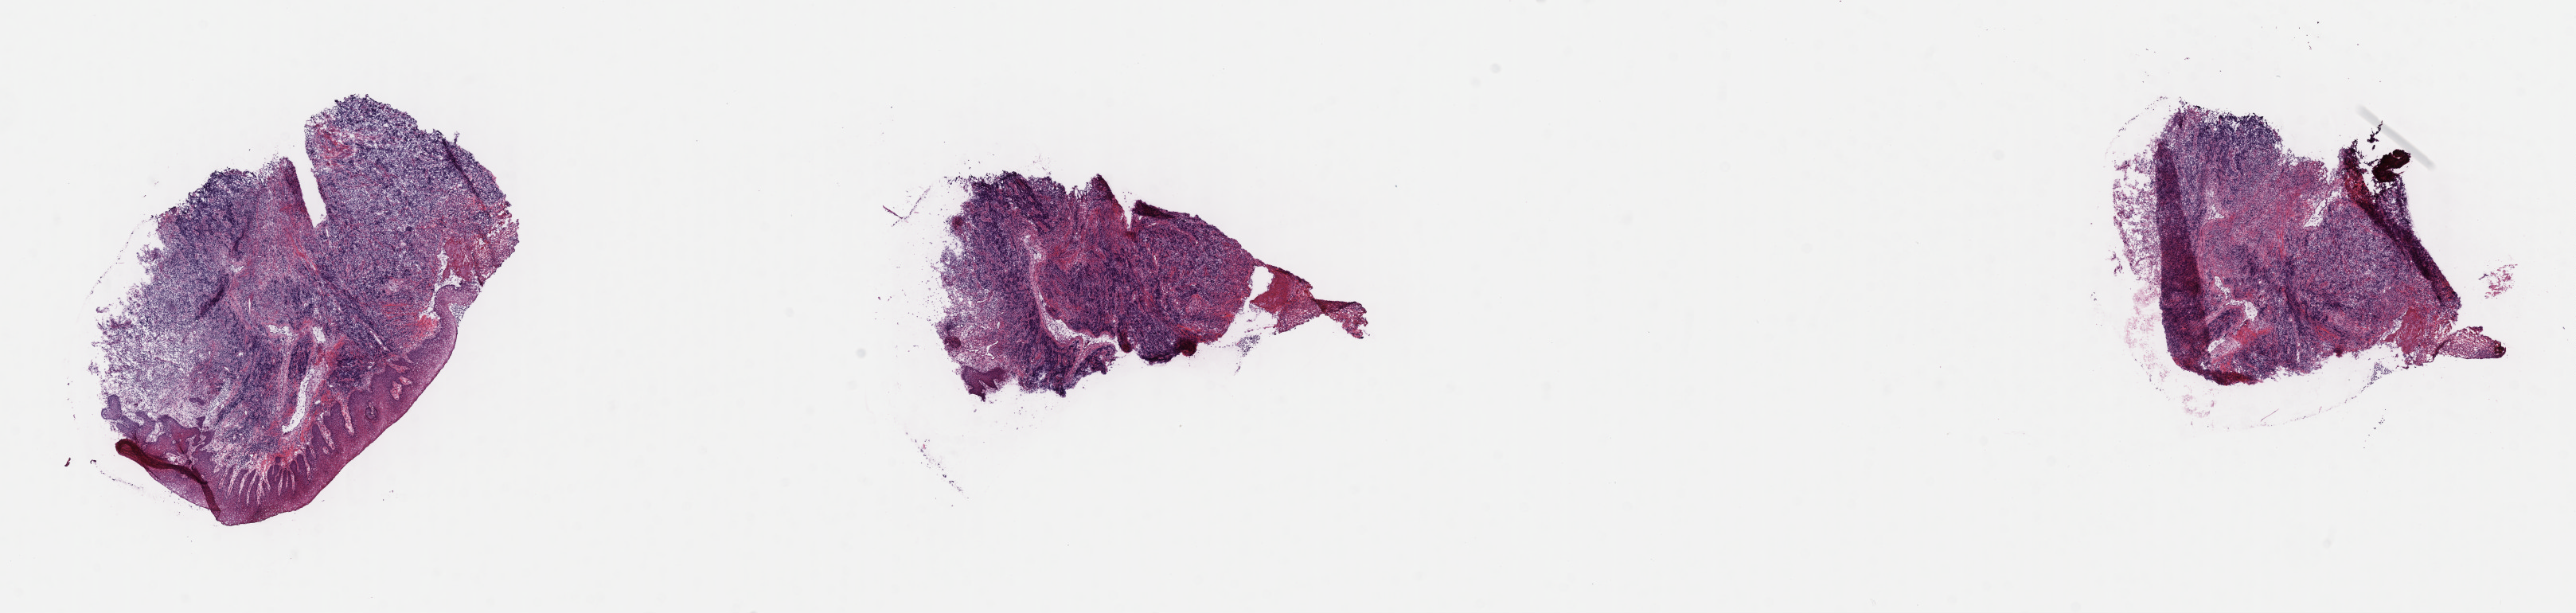
Whole-slide image, H&E stain, low-resolution overview of the scanned area, about 26.2 x 6.2 mm; frozen section (tissue freezing medium); primary tumor; anatomic site: cranium. Patient: male, age at initial diagnosis 6 years. Composition of this section per pathologist review: tumor cells 82%, tumor nuclei 90%, stromal cells 15%, necrosis 3%, normal cells 0%. Infiltration values recorded for this section: lymphocyte infiltration 3%, monocyte infiltration 3%, neutrophil infiltration 0%.
Section: top of the tissue portion. Ann Arbor stage (patient): Stage III. Diagnosis: Burkitt lymphoma, NOS.